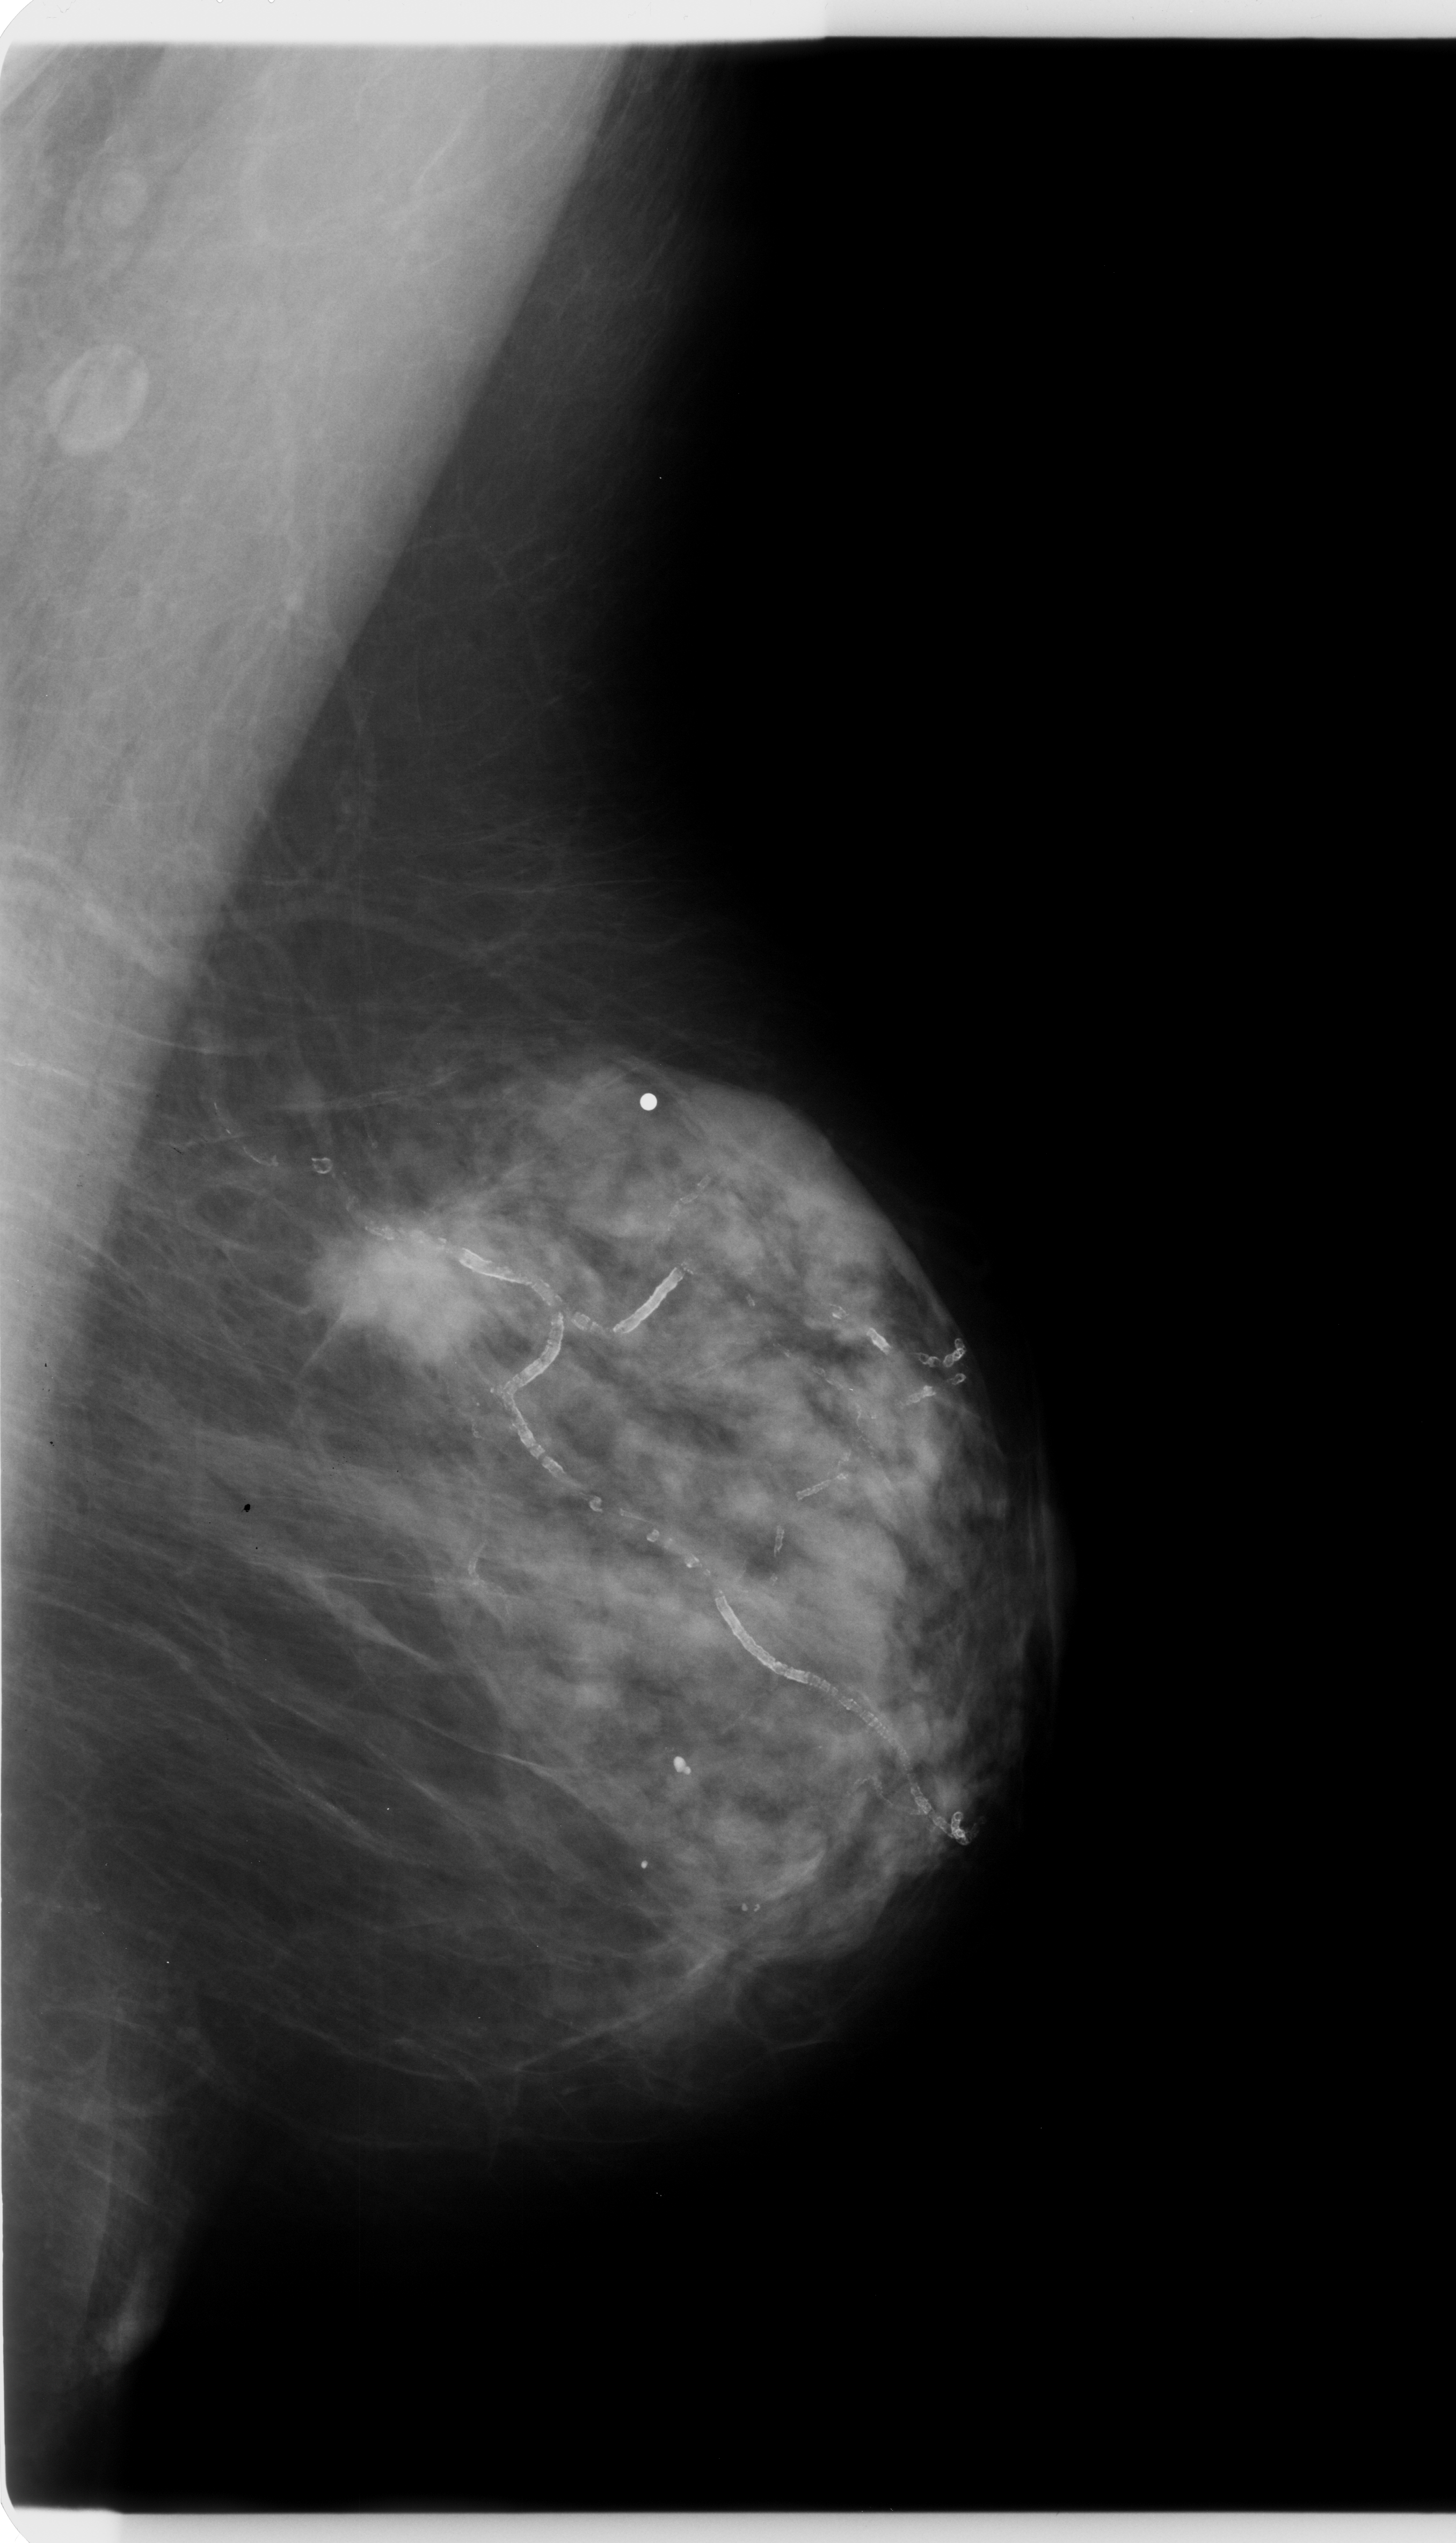
Digitized screen-film mammogram, left breast, mediolateral oblique (MLO) view, breast composition: scattered fibroglandular densities (BI-RADS density category 2 of 4).
Abnormality record for this image: mass, shape oval, margins spiculated; BI-RADS assessment category 5; pathology (as recorded): malignant.